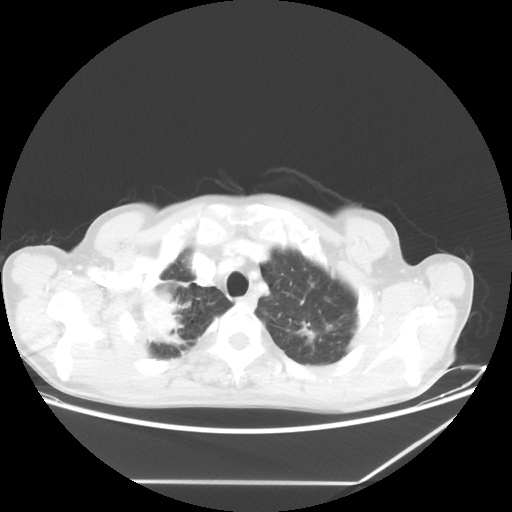
Chest CT, one axial slice; slice 56 of 65 in the series (ordered by position); reconstruction kernel STANDARD; 80 kVp; lung window (W 1500 / L -600 HU); 5 mm slice thickness; 512 × 512 image matrix, field of view 397 × 397 mm. Patient: male, 68 years. From the clinical record (not read from this slice): clinical TNM (as recorded): T3 N3 M0.
Outlined on this slice (rectangle marked by the reading radiologist):
- lung tumour (recorded histology: adenocarcinoma): bounding box [x1, y1, x2, y2] px = [128, 286, 187, 348]